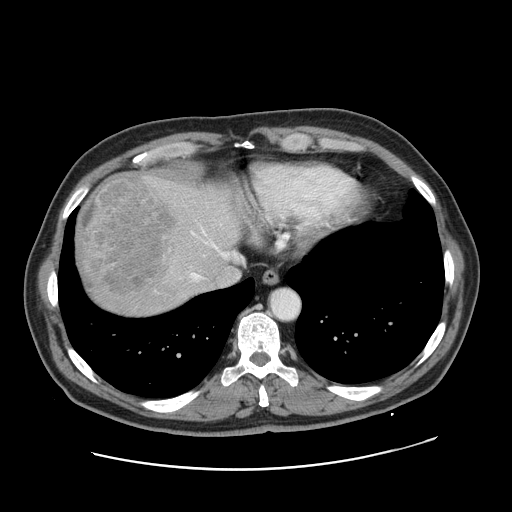
Contrast-enhanced abdominal CT, one axial slice. Slice 142 of 178 in the series (ordered by position). 120 kVp. Soft-tissue window (W 400 / L 40 HU). 2.5 mm slice thickness. 512 × 512 image matrix, field of view 403 × 403 mm. Male patient, age 63 years. From the clinical record (not read from this slice): diagnosis: colorectal cancer liver metastases, imaged before liver resection; multiple liver metastases: yes; largest metastasis: 8 cm.
Structures marked on this image (expert manual segmentation):
- hepatic veins: bounding box [x1, y1, x2, y2] px = [192, 232, 243, 278]
- liver: [76, 171, 241, 317]
- planned liver remnant (the part of the liver to remain after resection): [180, 182, 242, 276]
- liver metastasis: [78, 176, 174, 293]